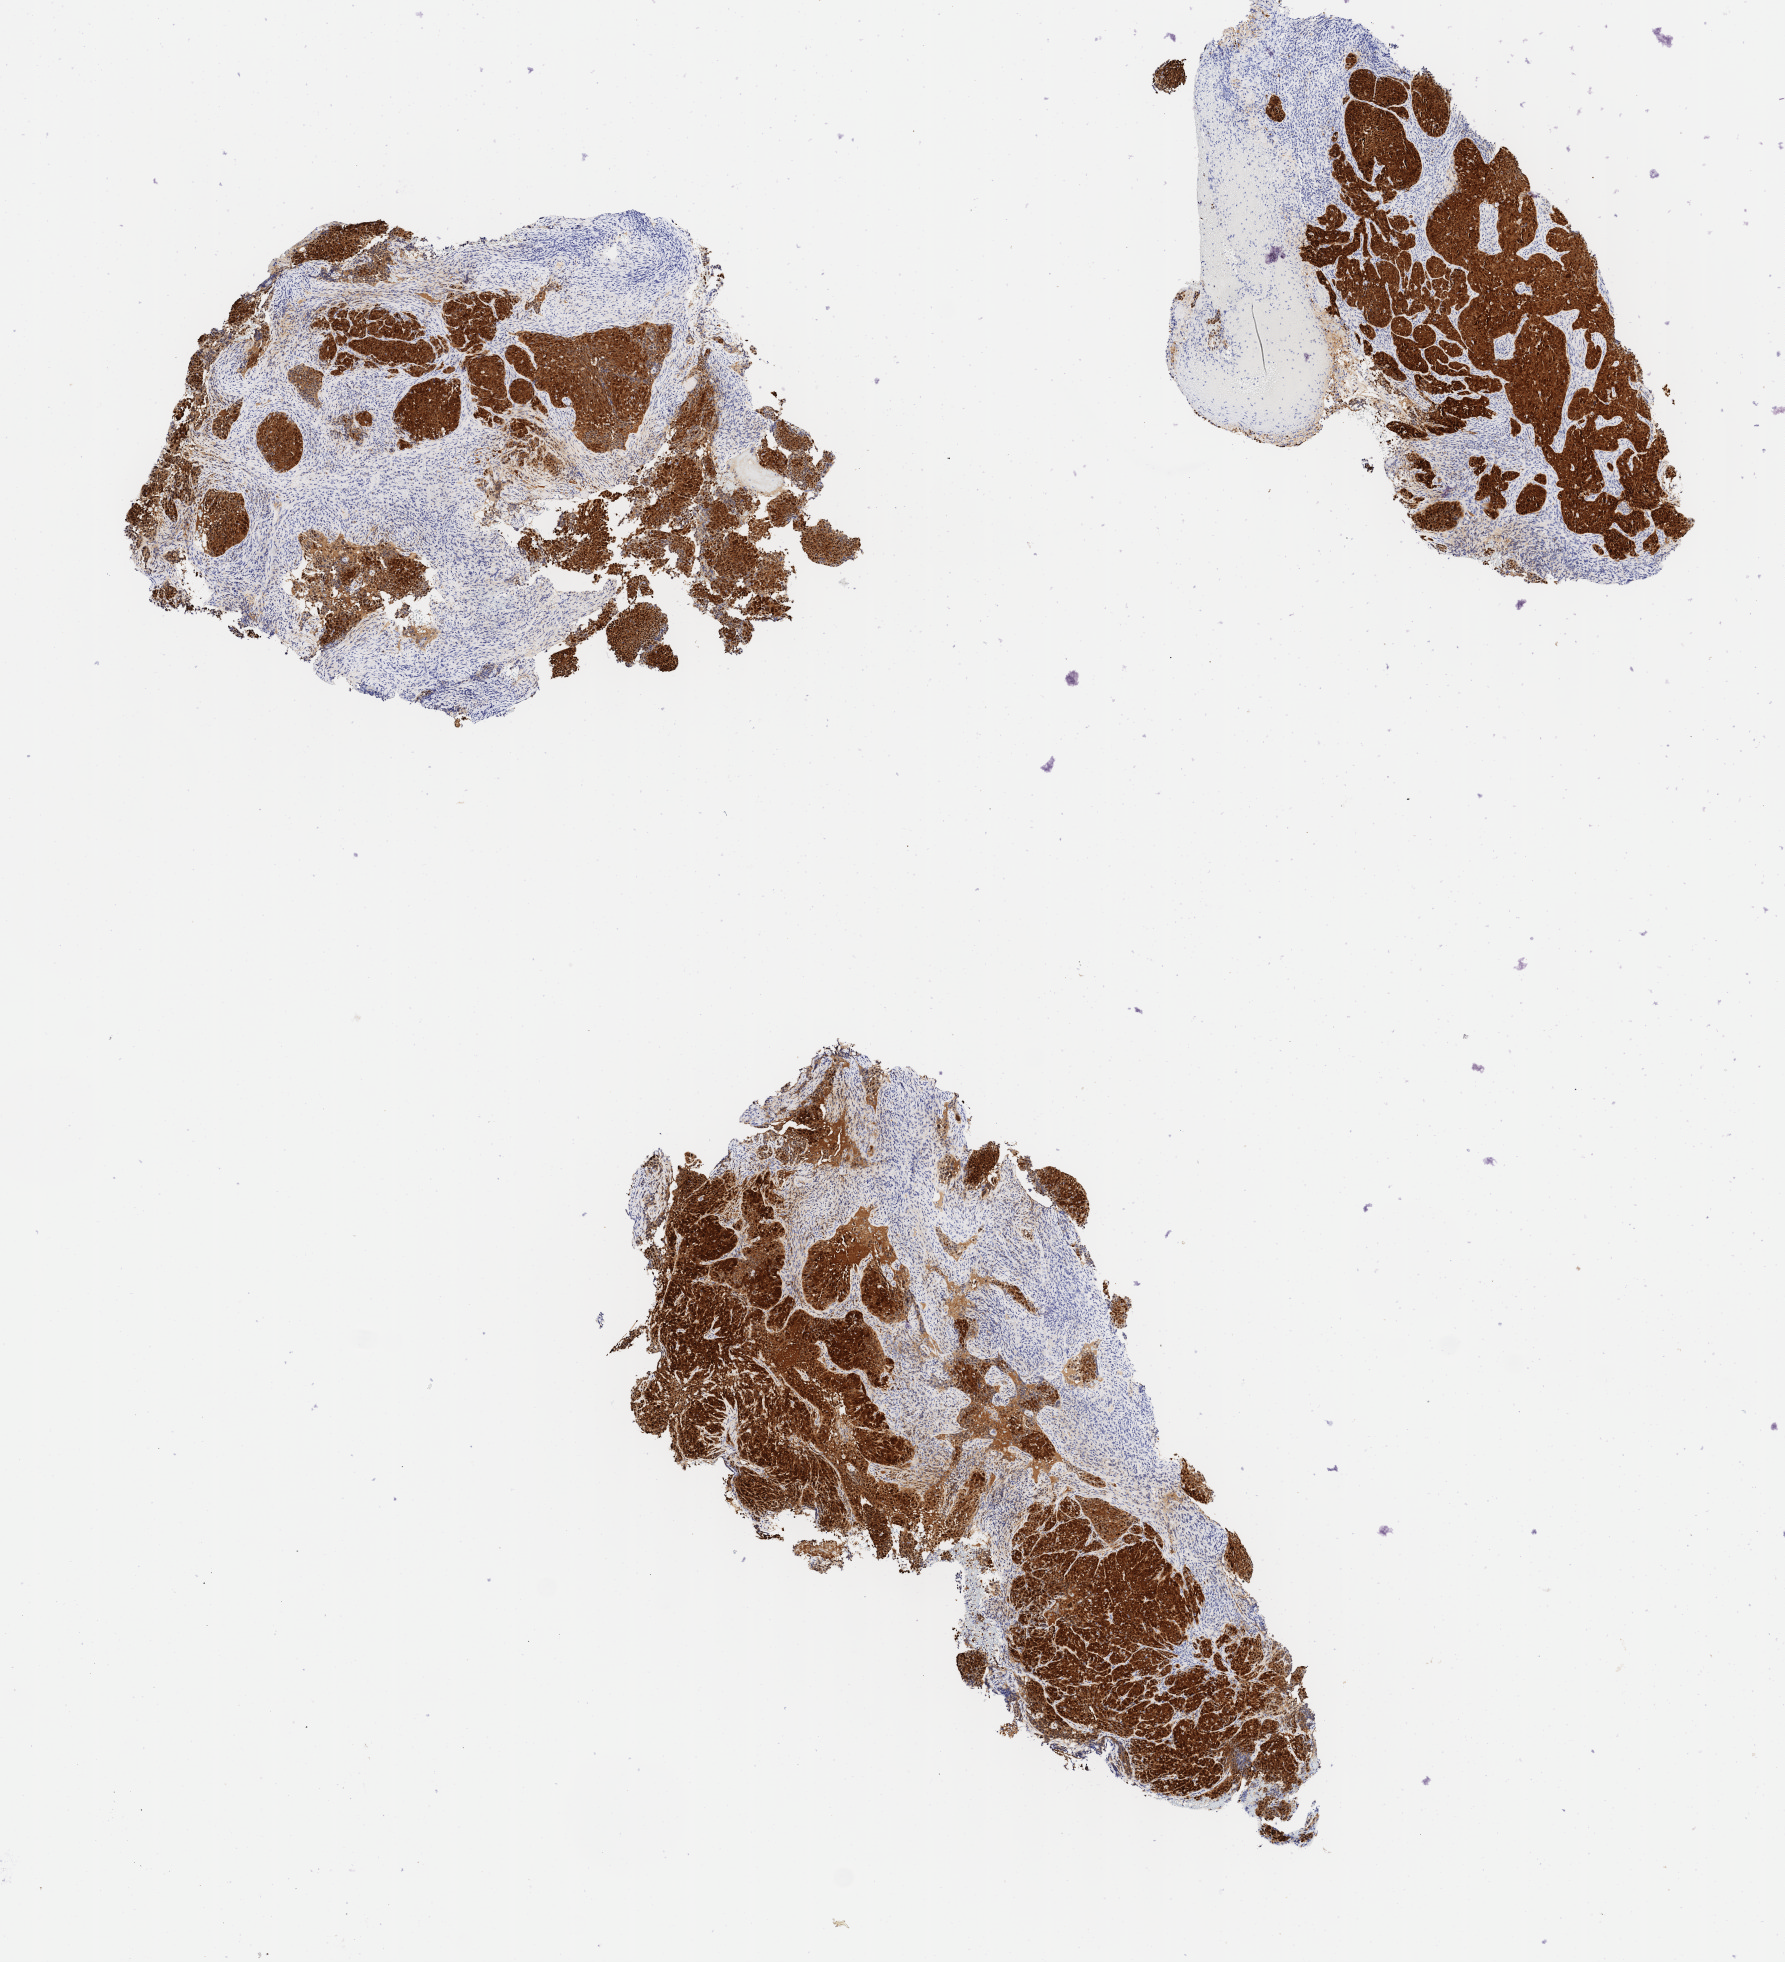
IHC for p16 (p16INK4a), whole-slide image, a low-resolution overview of the entire scanned area, about 7.1 x 7.8 mm. Specimen: tumor tissue. Anatomic site: cervix. Patient: female, 34 years old.
Histologic diagnosis: Squamous cell carcinoma, large cell, nonkeratinizing, NOS.